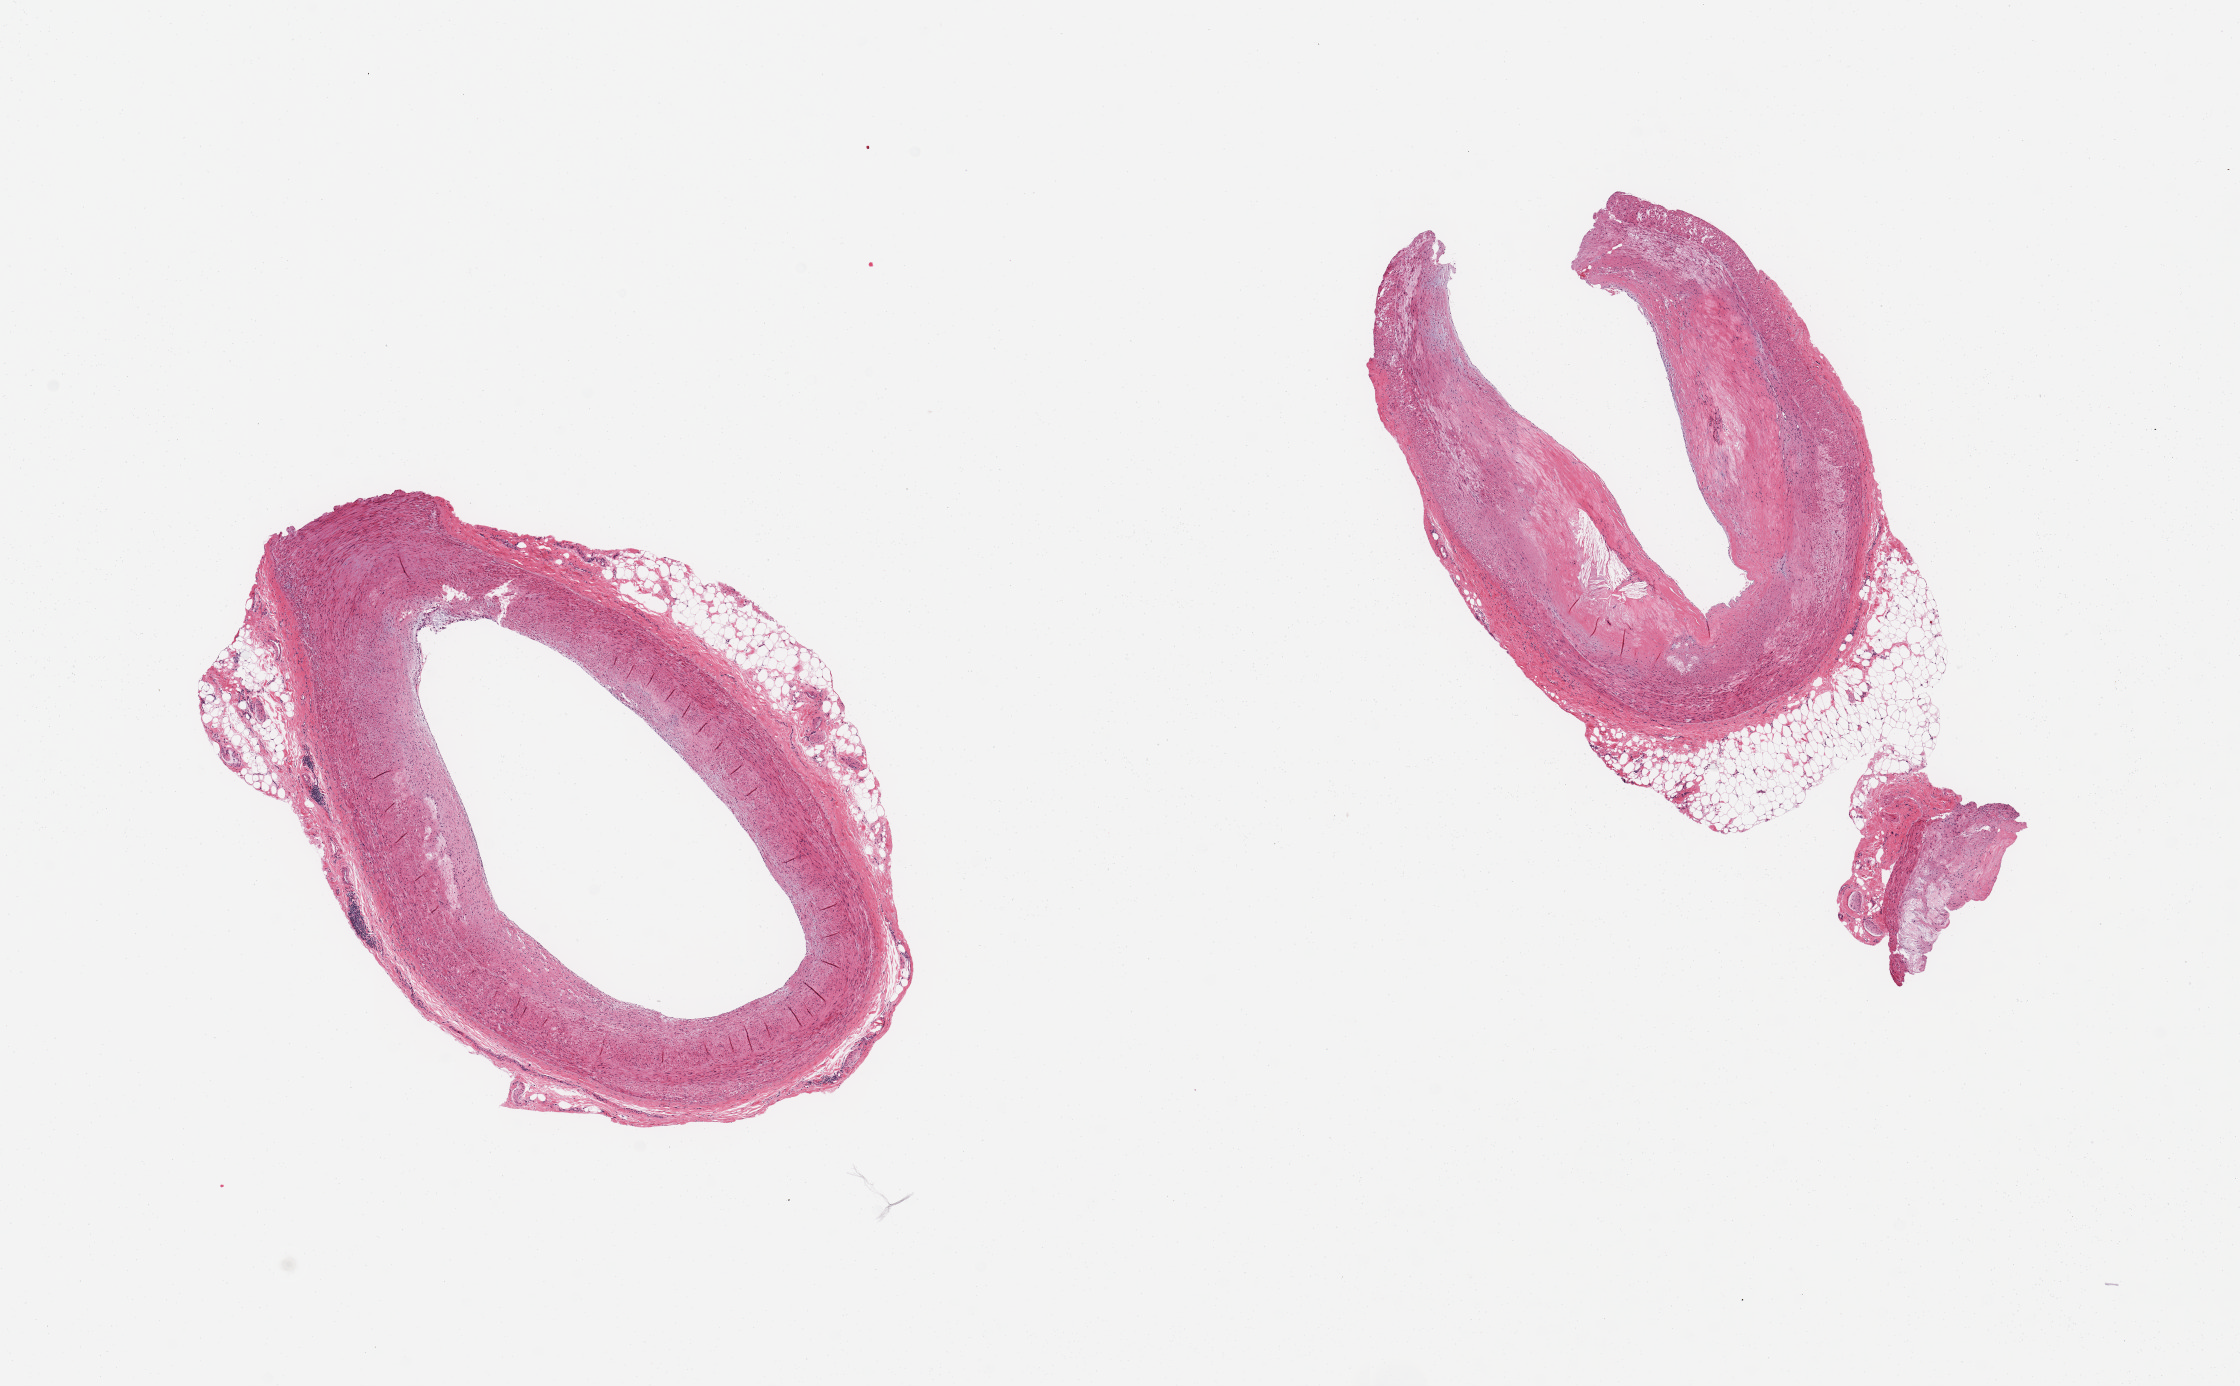
Whole-slide image, H&E stain, a low-resolution overview of the entire scanned area, about 17.7 x 11.0 mm (slide scanned at 20x), PAXgene-fixed, paraffin-embedded tissue, section of coronary artery (target tissue), tissue donor sample. Male donor.
Pathologist's review note for this sample: 2 pieces; atheromatous plaques of mild and moderate degree; perivascular fat eccentrically.